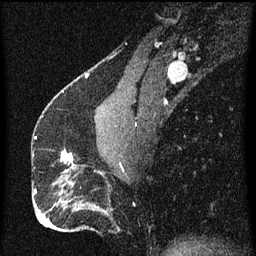
Breast MRI (dynamic contrast-enhanced), one sagittal slice. Slice 28 of 60 in the series (ordered by position). Dynamic contrast-enhanced series, image 2 of 3 at this slice position (ordered by acquisition). 1.5 T. TE 4.2 ms, TR 8 ms. 2 mm slice thickness. 256 × 256 image matrix, field of view 180 × 180 mm. Female patient, age 51 years.
Outlined on this slice (semi-automatic segmentation, software-assisted and operator-edited):
- analysis volume of interest (the breast-tissue region the enhancement analysis was run in; not a lesion): bounding box [x1, y1, x2, y2] px = [62, 150, 85, 175]
- tumour enhancement mask (voxels above the 70 % enhancement threshold inside the analysis volume of interest): [62, 150, 73, 173]